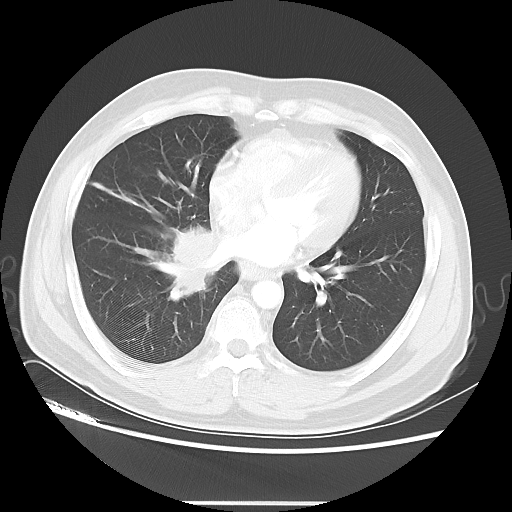
Chest CT, one axial slice; slice 18 of 48 in the series (ordered by position); reconstruction kernel LUNG; 120 kVp; lung window (W 1500 / L -600 HU); 5 mm slice thickness; 512 × 512 image matrix, field of view 390 × 390 mm. Patient: male, 53 years. Case-level facts recorded for this patient, not image findings: clinical TNM (as recorded): T2 N3 M0; histopathological grade: G3.
Structures marked on this image (bounding box drawn by a radiologist):
- lung tumour (recorded histology: small cell carcinoma): bounding box <157,217,230,312> (left, top, right, bottom; pixels)